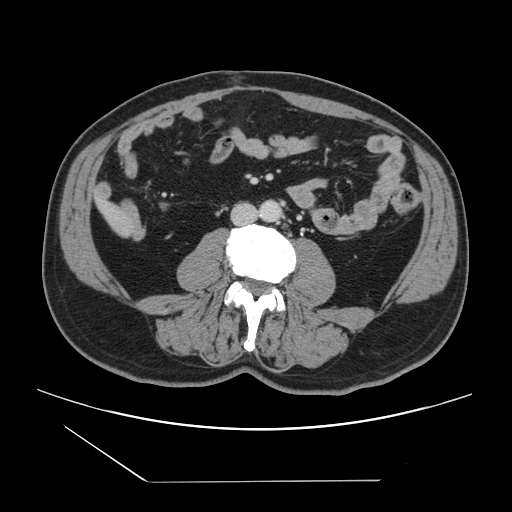
Contrast-enhanced abdominal CT, one axial slice; slice 13 of 157 in the series (ordered by position); 120 kVp; intravenous contrast given; soft-tissue window (W 400 / L 40 HU); 2.5 mm slice thickness; 512 × 512 image matrix, field of view 407 × 407 mm. Male patient, age 61 years. Case-level facts recorded for this patient, not image findings: diagnosis: colorectal cancer liver metastases, imaged before liver resection; multiple liver metastases: yes; largest metastasis: 5.5 cm; disease in both lobes: yes.
Annotated regions visible in this slice (manually delineated by an expert):
- liver: bounding box (x1, y1, x2, y2) in pixels: (99, 202, 130, 235)
- planned liver remnant (the part of the liver to remain after resection): (99, 201, 118, 216)